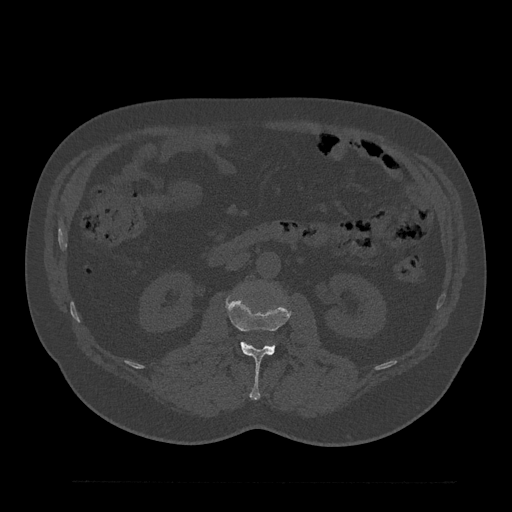
CT including the spine, one axial slice. Slice 88 of 797 in the series (ordered by position). Reconstruction kernel Br40s/3. 120 kVp. Bone window (W 1800 / L 400 HU). 0.5 mm slice thickness. 512 × 512 image matrix. Male patient, age 61 years. Case-level facts recorded for this patient, not image findings: primary cancer: prostate.
Annotated regions visible in this slice (semi-automatic segmentation, software-assisted and operator-edited):
- L2 vertebra: bounding box (x1, y1, x2, y2) in pixels: (226, 296, 291, 400)